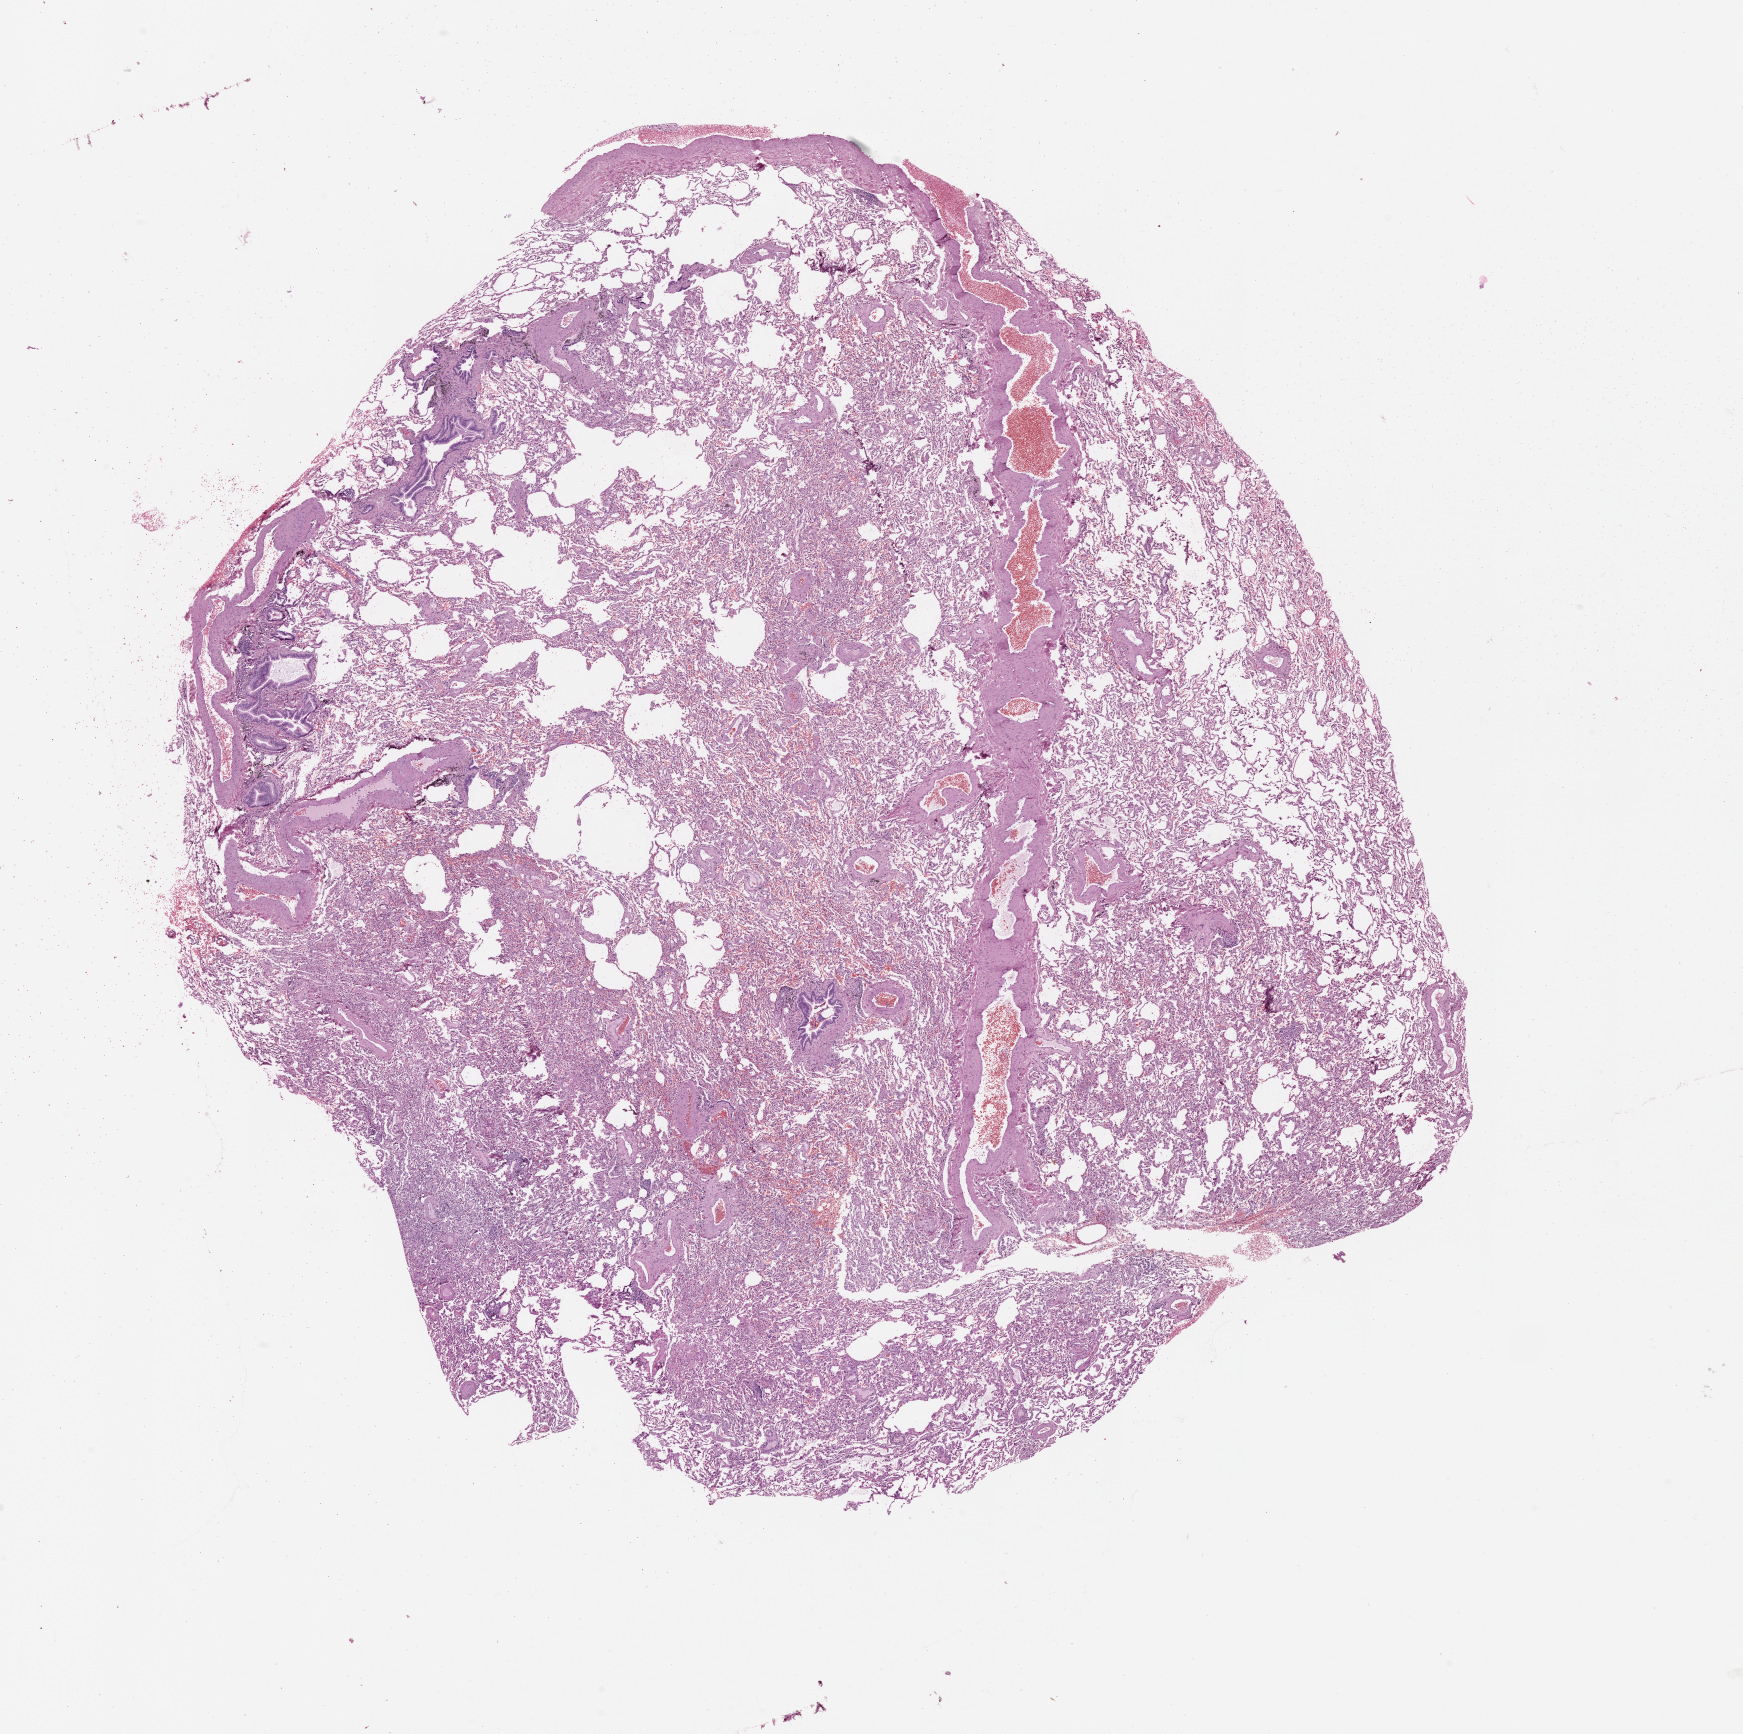
H&E-stained whole-slide image — a low-resolution overview of the entire scanned area, about 14.0 x 14.0 mm. Lung, normal (non-tumour) tissue. 63-year-old male patient.
* this section: normal (non-tumour) tissue from the same patient
* patient diagnosis (cohort enrolment): squamous cell carcinoma (lung)